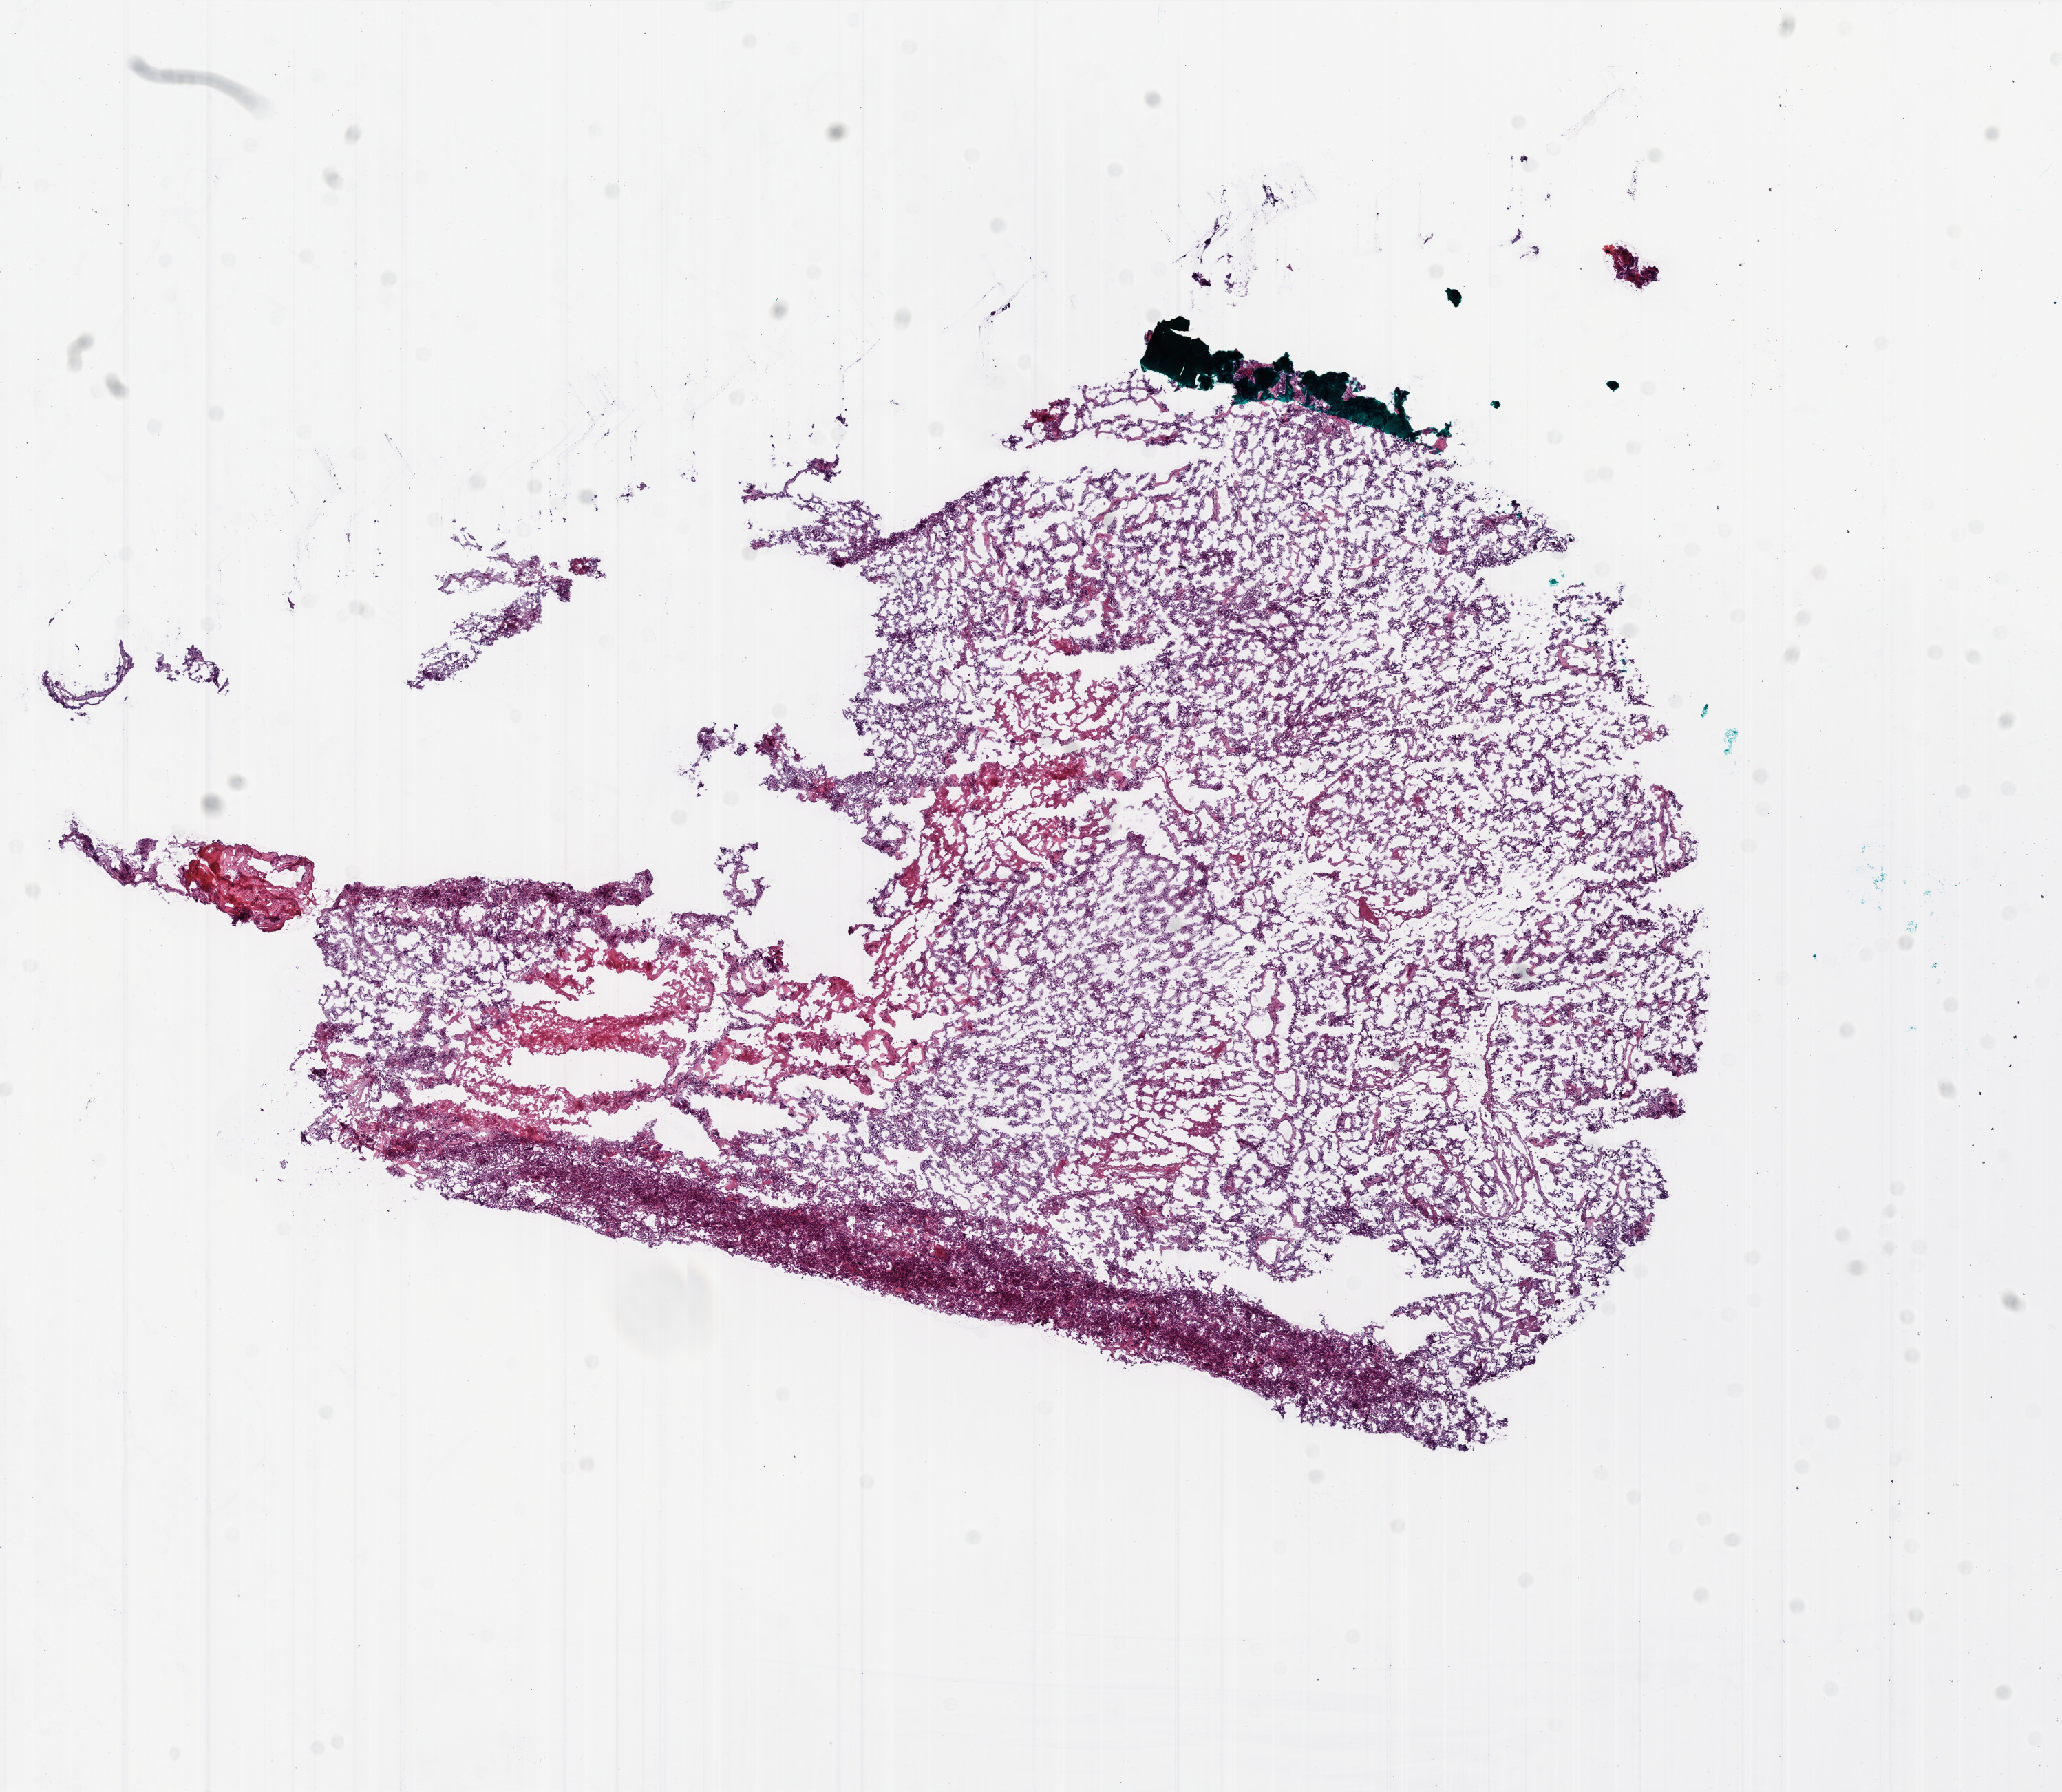
Hematoxylin and eosin (H&E) stained whole-slide image — a low-resolution overview of the entire scanned area, about 12.0 x 10.4 mm (slide scanned at 20x). Frozen section from the bottom of the tissue portion. Sample: primary tumour, brain. Patient: male, age at initial diagnosis 26 years. Slide review estimates, as recorded: tumour cells 80%, tumour nuclei 100%, normal cells 0%, stromal cells 0%, necrosis 20%. Infiltration values recorded for this section: lymphocyte infiltration 0%.
Pathologic diagnosis: Glioblastoma.